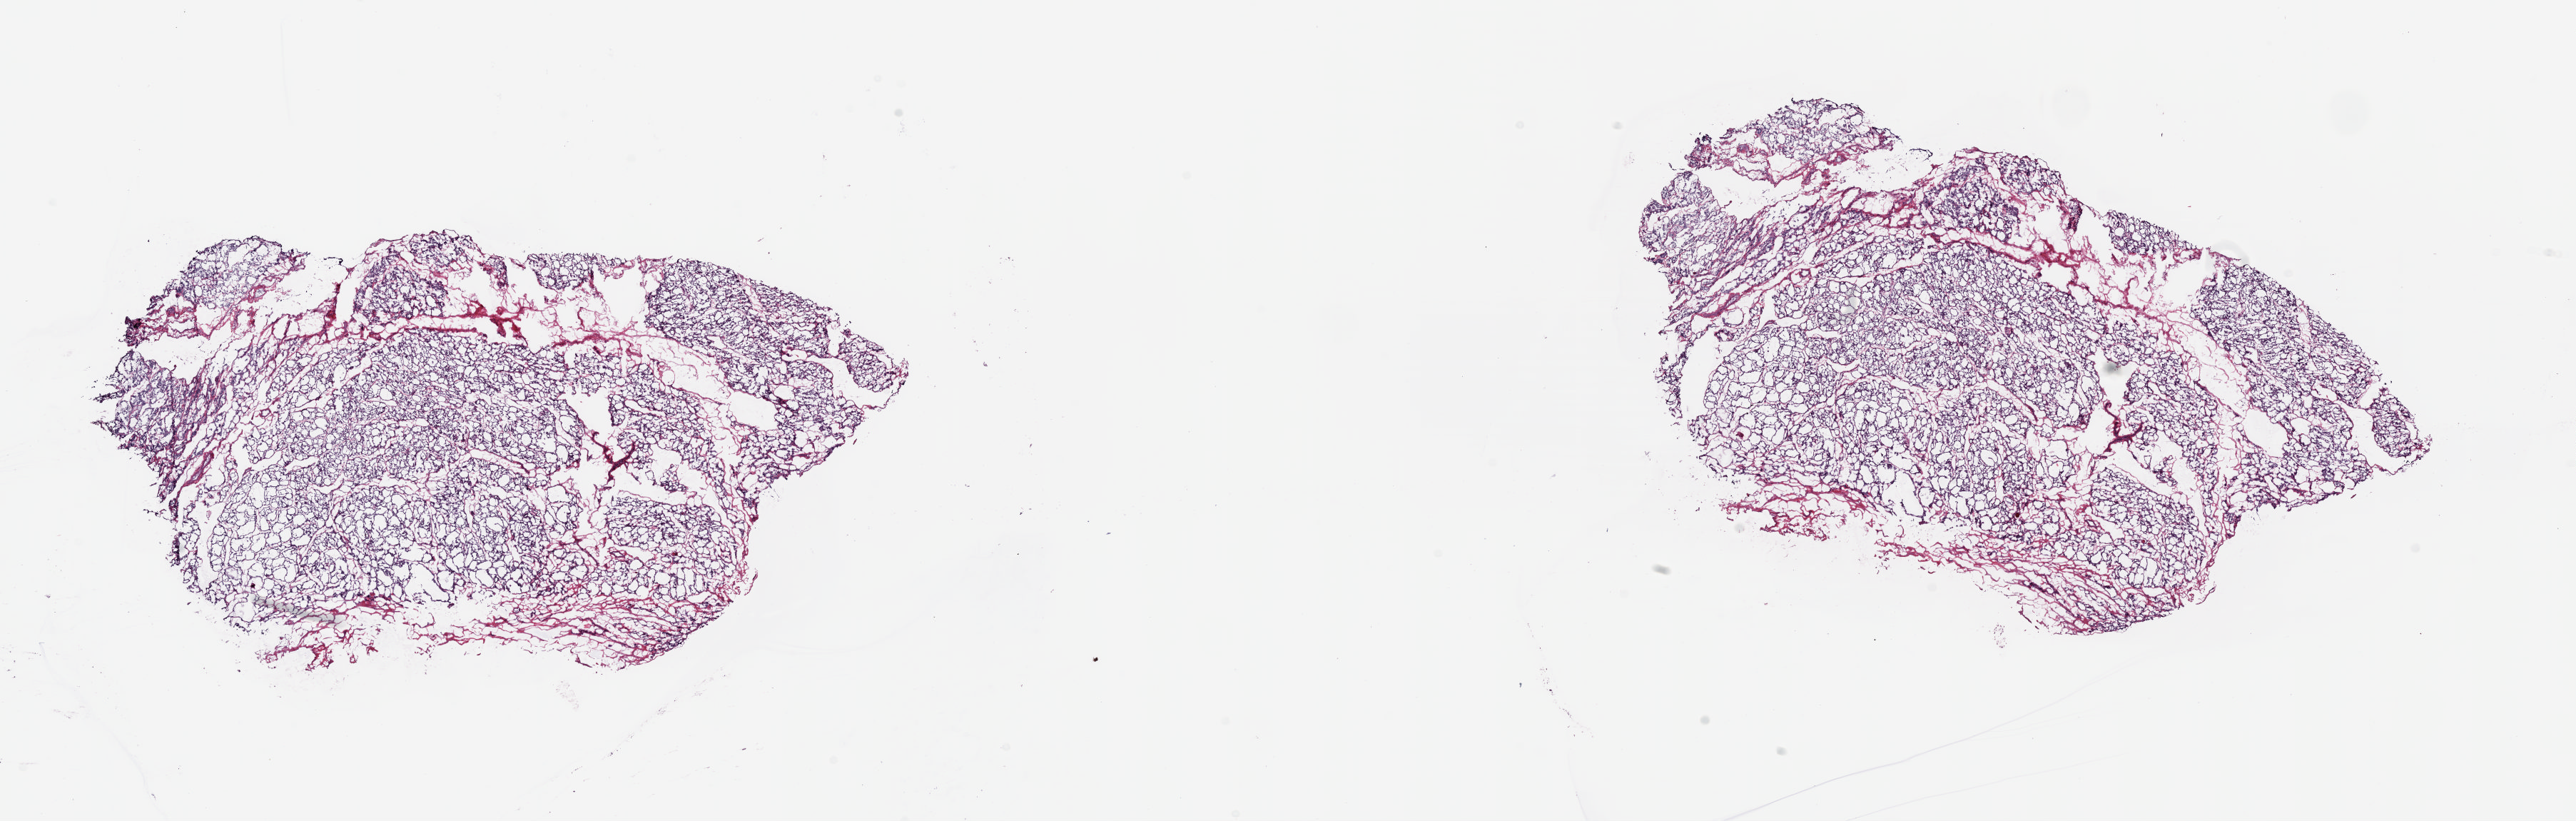
Digitized H&E-stained tissue section (whole slide) — a low-resolution overview of the entire scanned area, about 28.5 x 9.1 mm (from a 20x scan); frozen section; solid tissue normal (non-tumour tissue) sample from the thyroid. Female patient; age at initial diagnosis 47 years.
This section: solid tissue normal (non-tumour) sample from the same patient. Patient diagnosis: Papillary adenocarcinoma, NOS (thyroid gland).